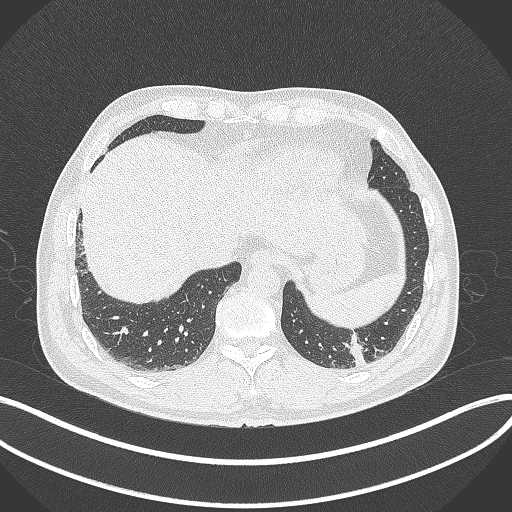
Chest CT, one axial slice. Position 53 of 300 along the scan axis. 120 kVp. Lung window (W 1500 / L -600 HU). 1 mm slice thickness. 512 × 512 image matrix. Patient: male, 54 years. From the clinical record (not read from this slice): clinical TNM (as recorded): T1c N0 M1; histopathological grade: G3.
Structures marked on this image (bounding box drawn by a radiologist):
- lung tumour (recorded histology: adenocarcinoma): bounding box (x1, y1, x2, y2) in pixels: (343, 327, 371, 372)